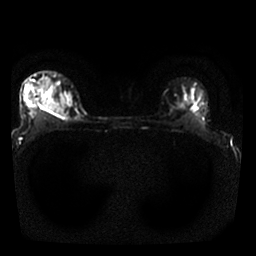
Breast MRI, one axial slice. Position 21 of 25 along the scan axis. Diffusion-weighted series; image 2 of 4 stored at this slice position (different b-values; order by instance number). 1.5 T. 4 mm slice thickness. 256 × 256 image matrix, field of view 310 × 310 mm. Female patient.
Structures marked on this image (expert manual segmentation):
- tumour on diffusion-weighted imaging: bounding box (x1, y1, x2, y2) in pixels: (46, 102, 62, 115)